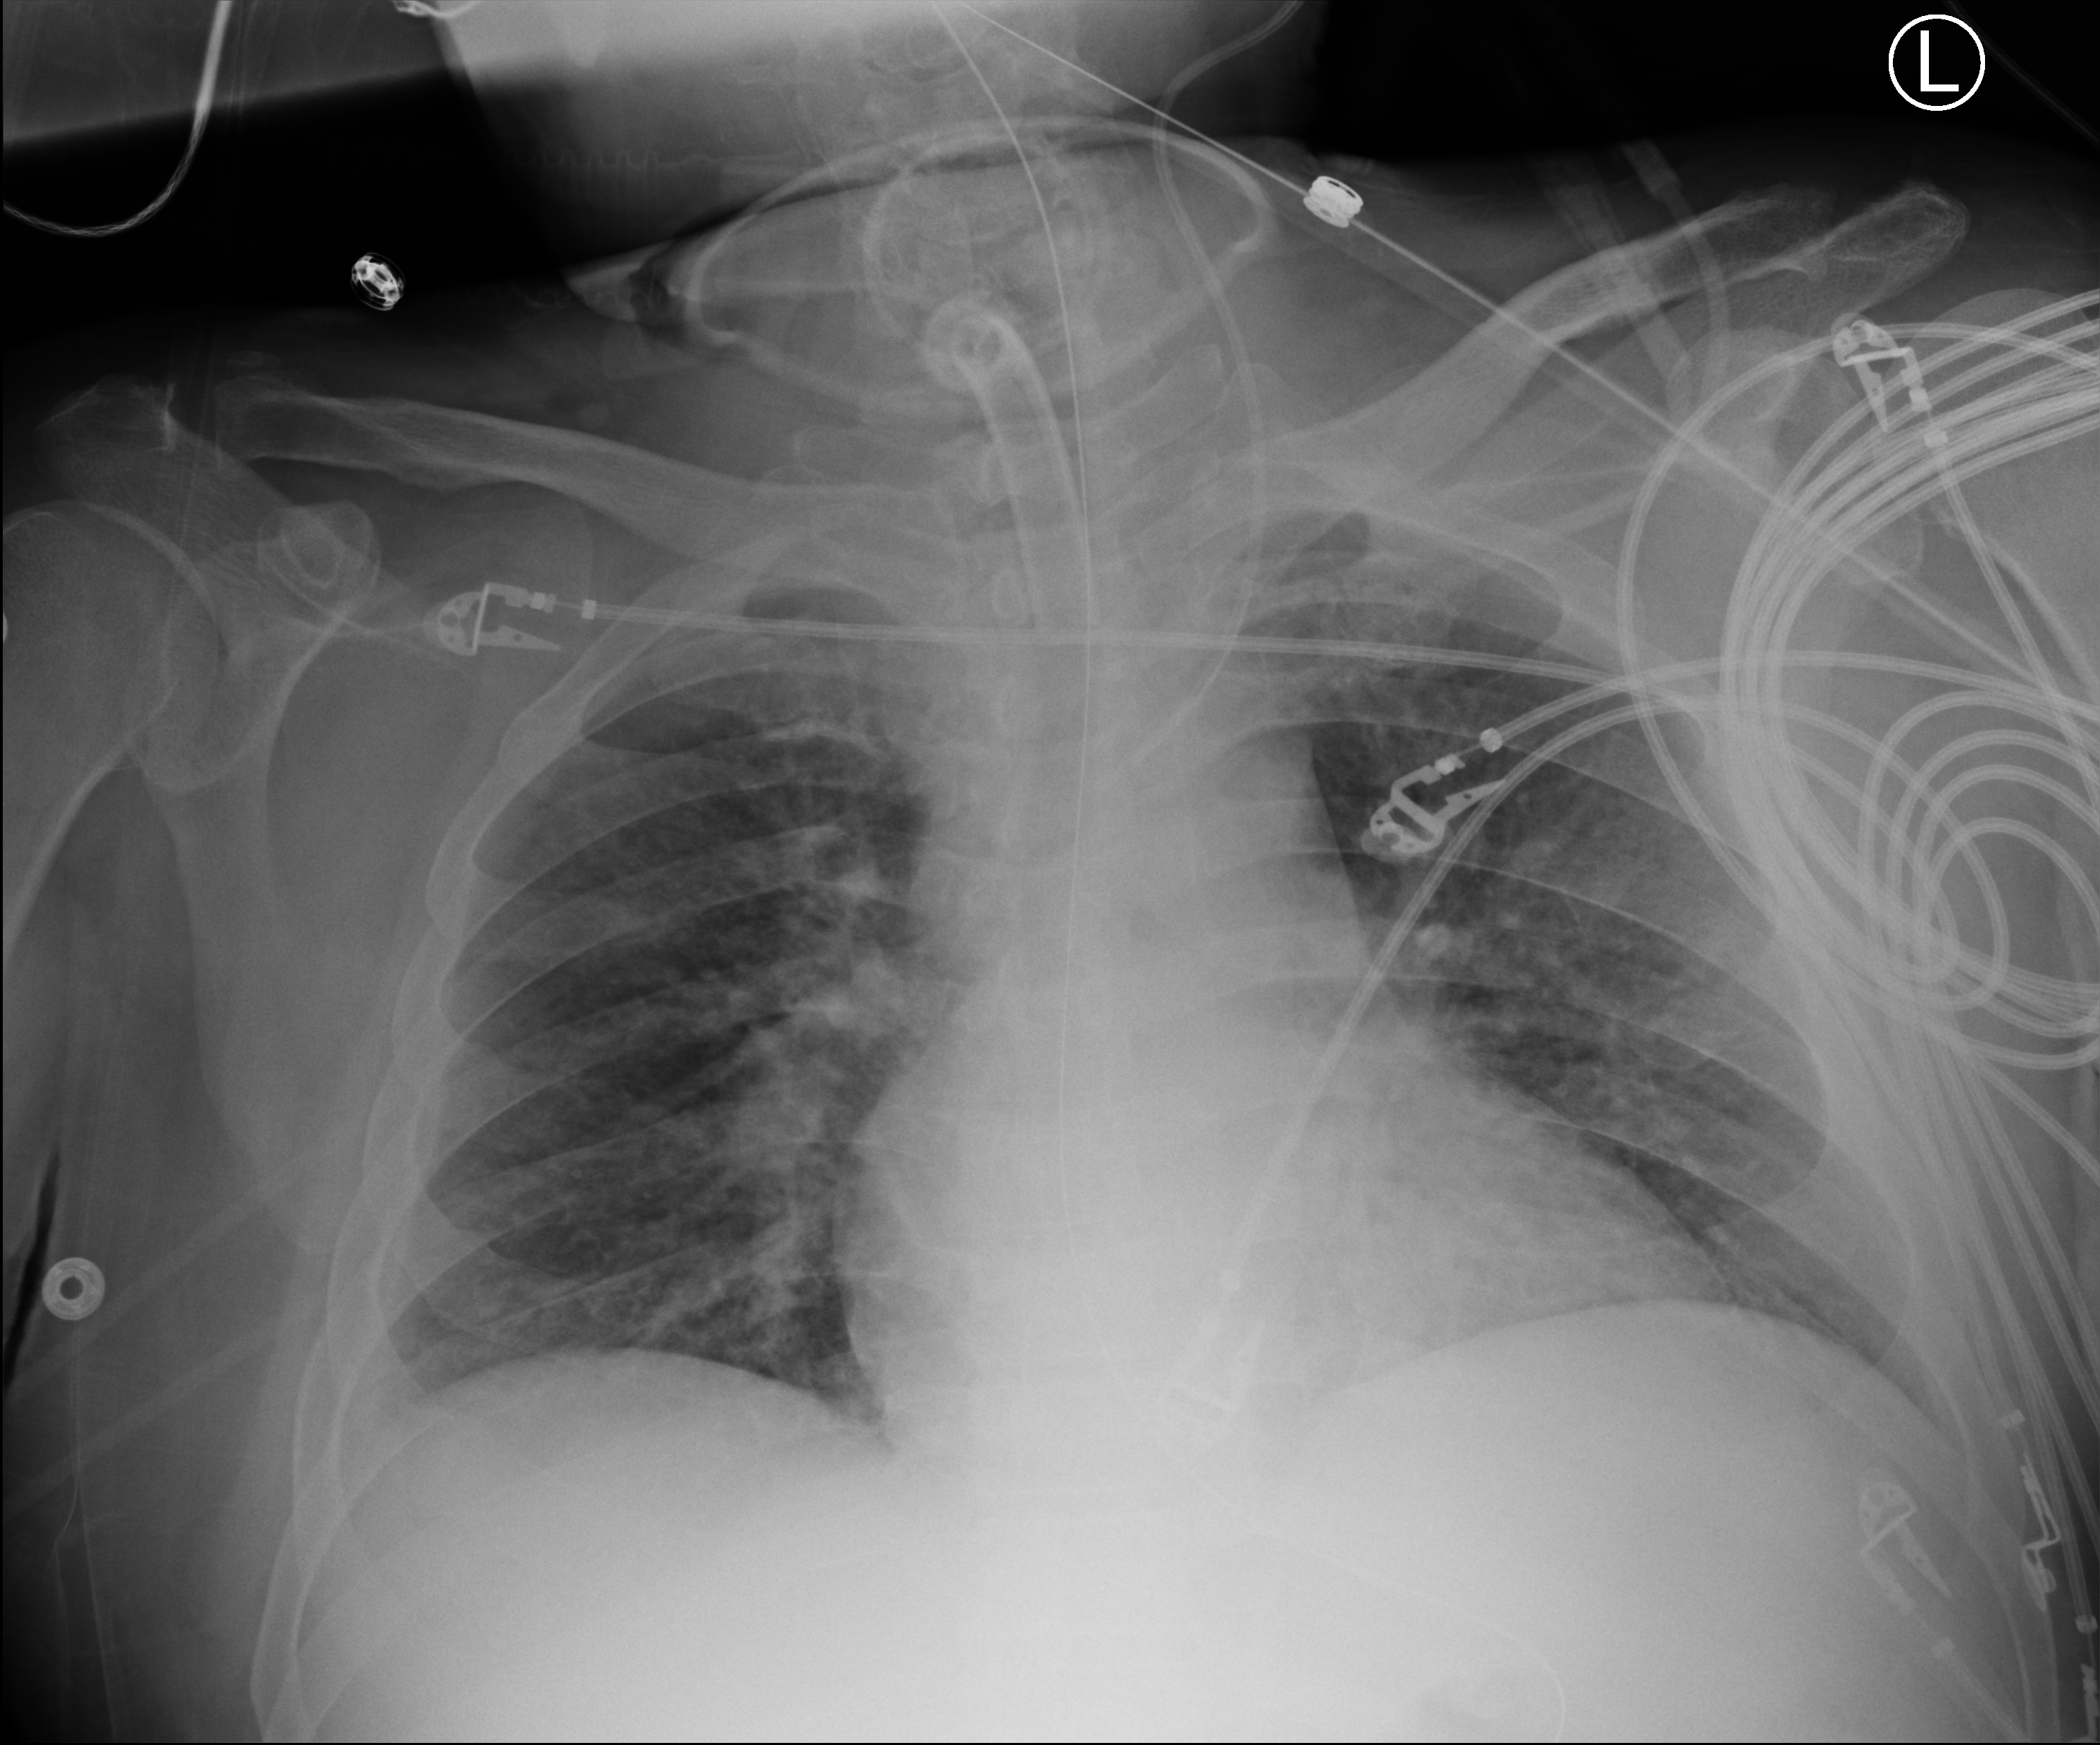
Portable chest radiograph, anteroposterior (AP) projection. Patient hospitalised with COVID-19; male, aged 18–59 years.
Hospital-stay facts (about this admission, not read from this image; timing relative to this image not recorded):
- mechanically ventilated during this hospital stay: yes